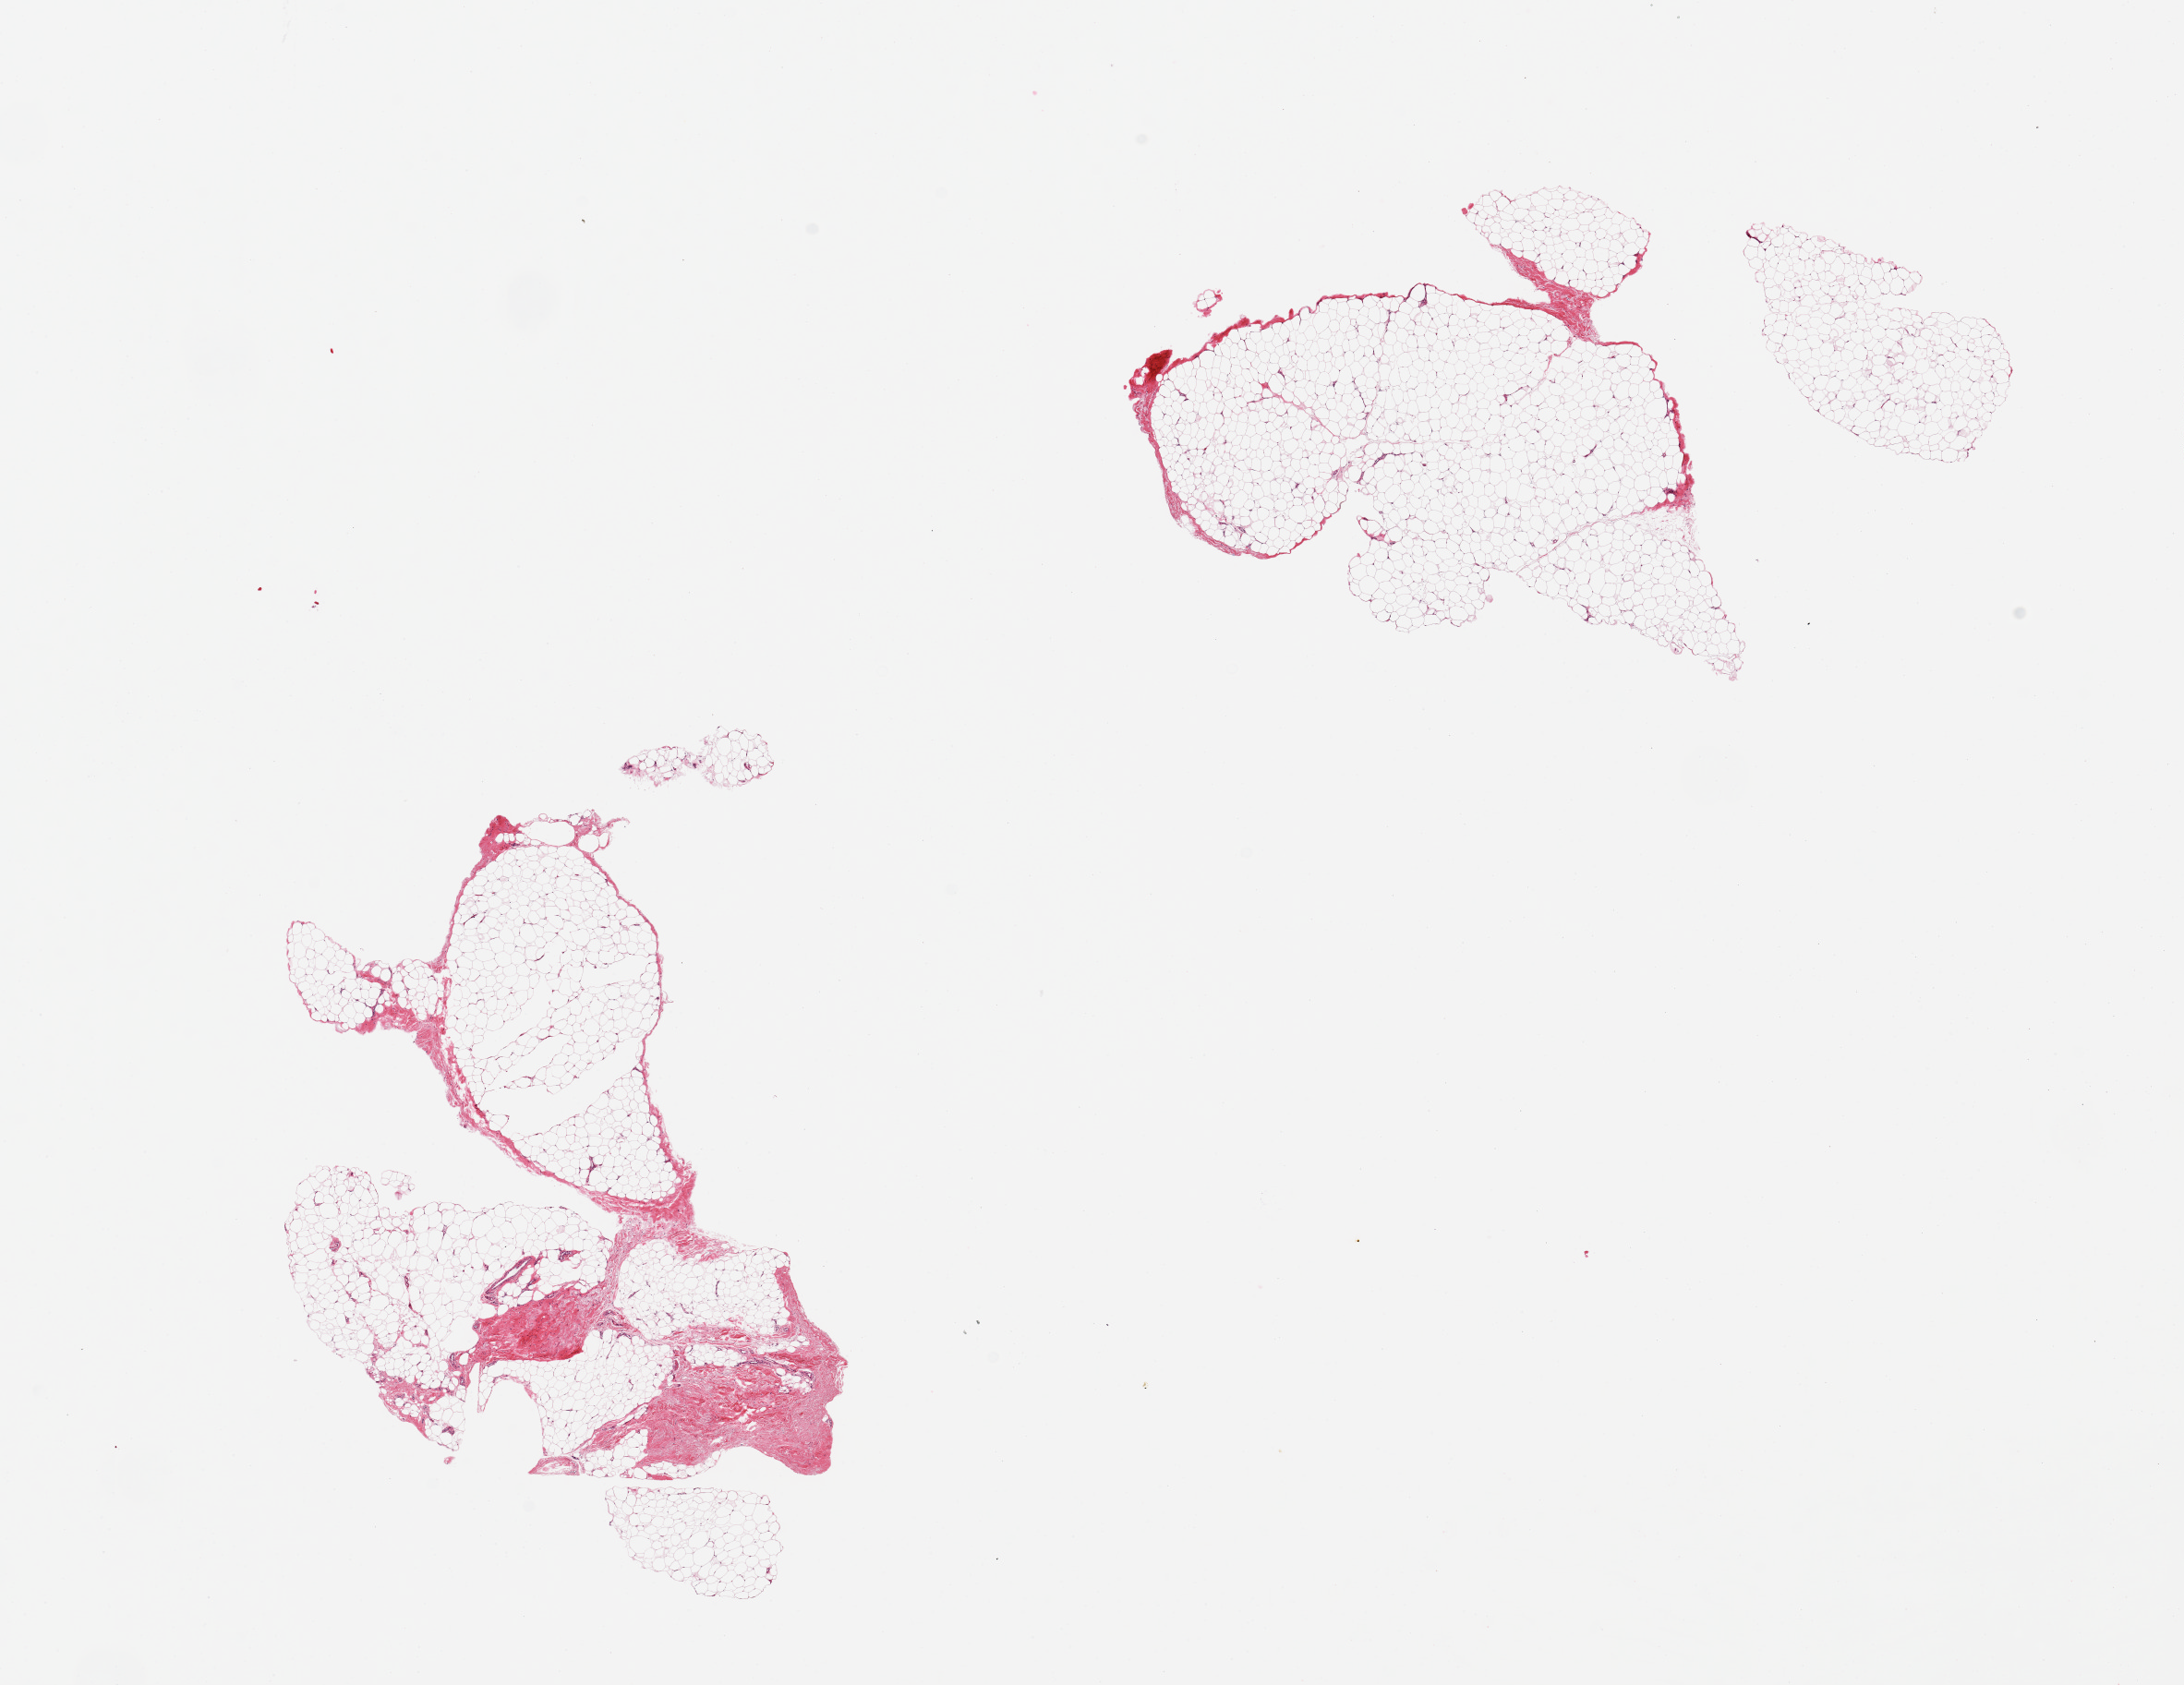
Haematoxylin and eosin whole-slide image — low-resolution overview of the scanned area, about 18.7 x 14.4 mm (from a 20x scan); PAXgene-fixed paraffin-embedded (PFPE) section; sampled site (target tissue): adipose tissue; tissue donor sample.
Review note (as recorded): 2 pieces fascia/fibrous tissue is ~10-15% total.